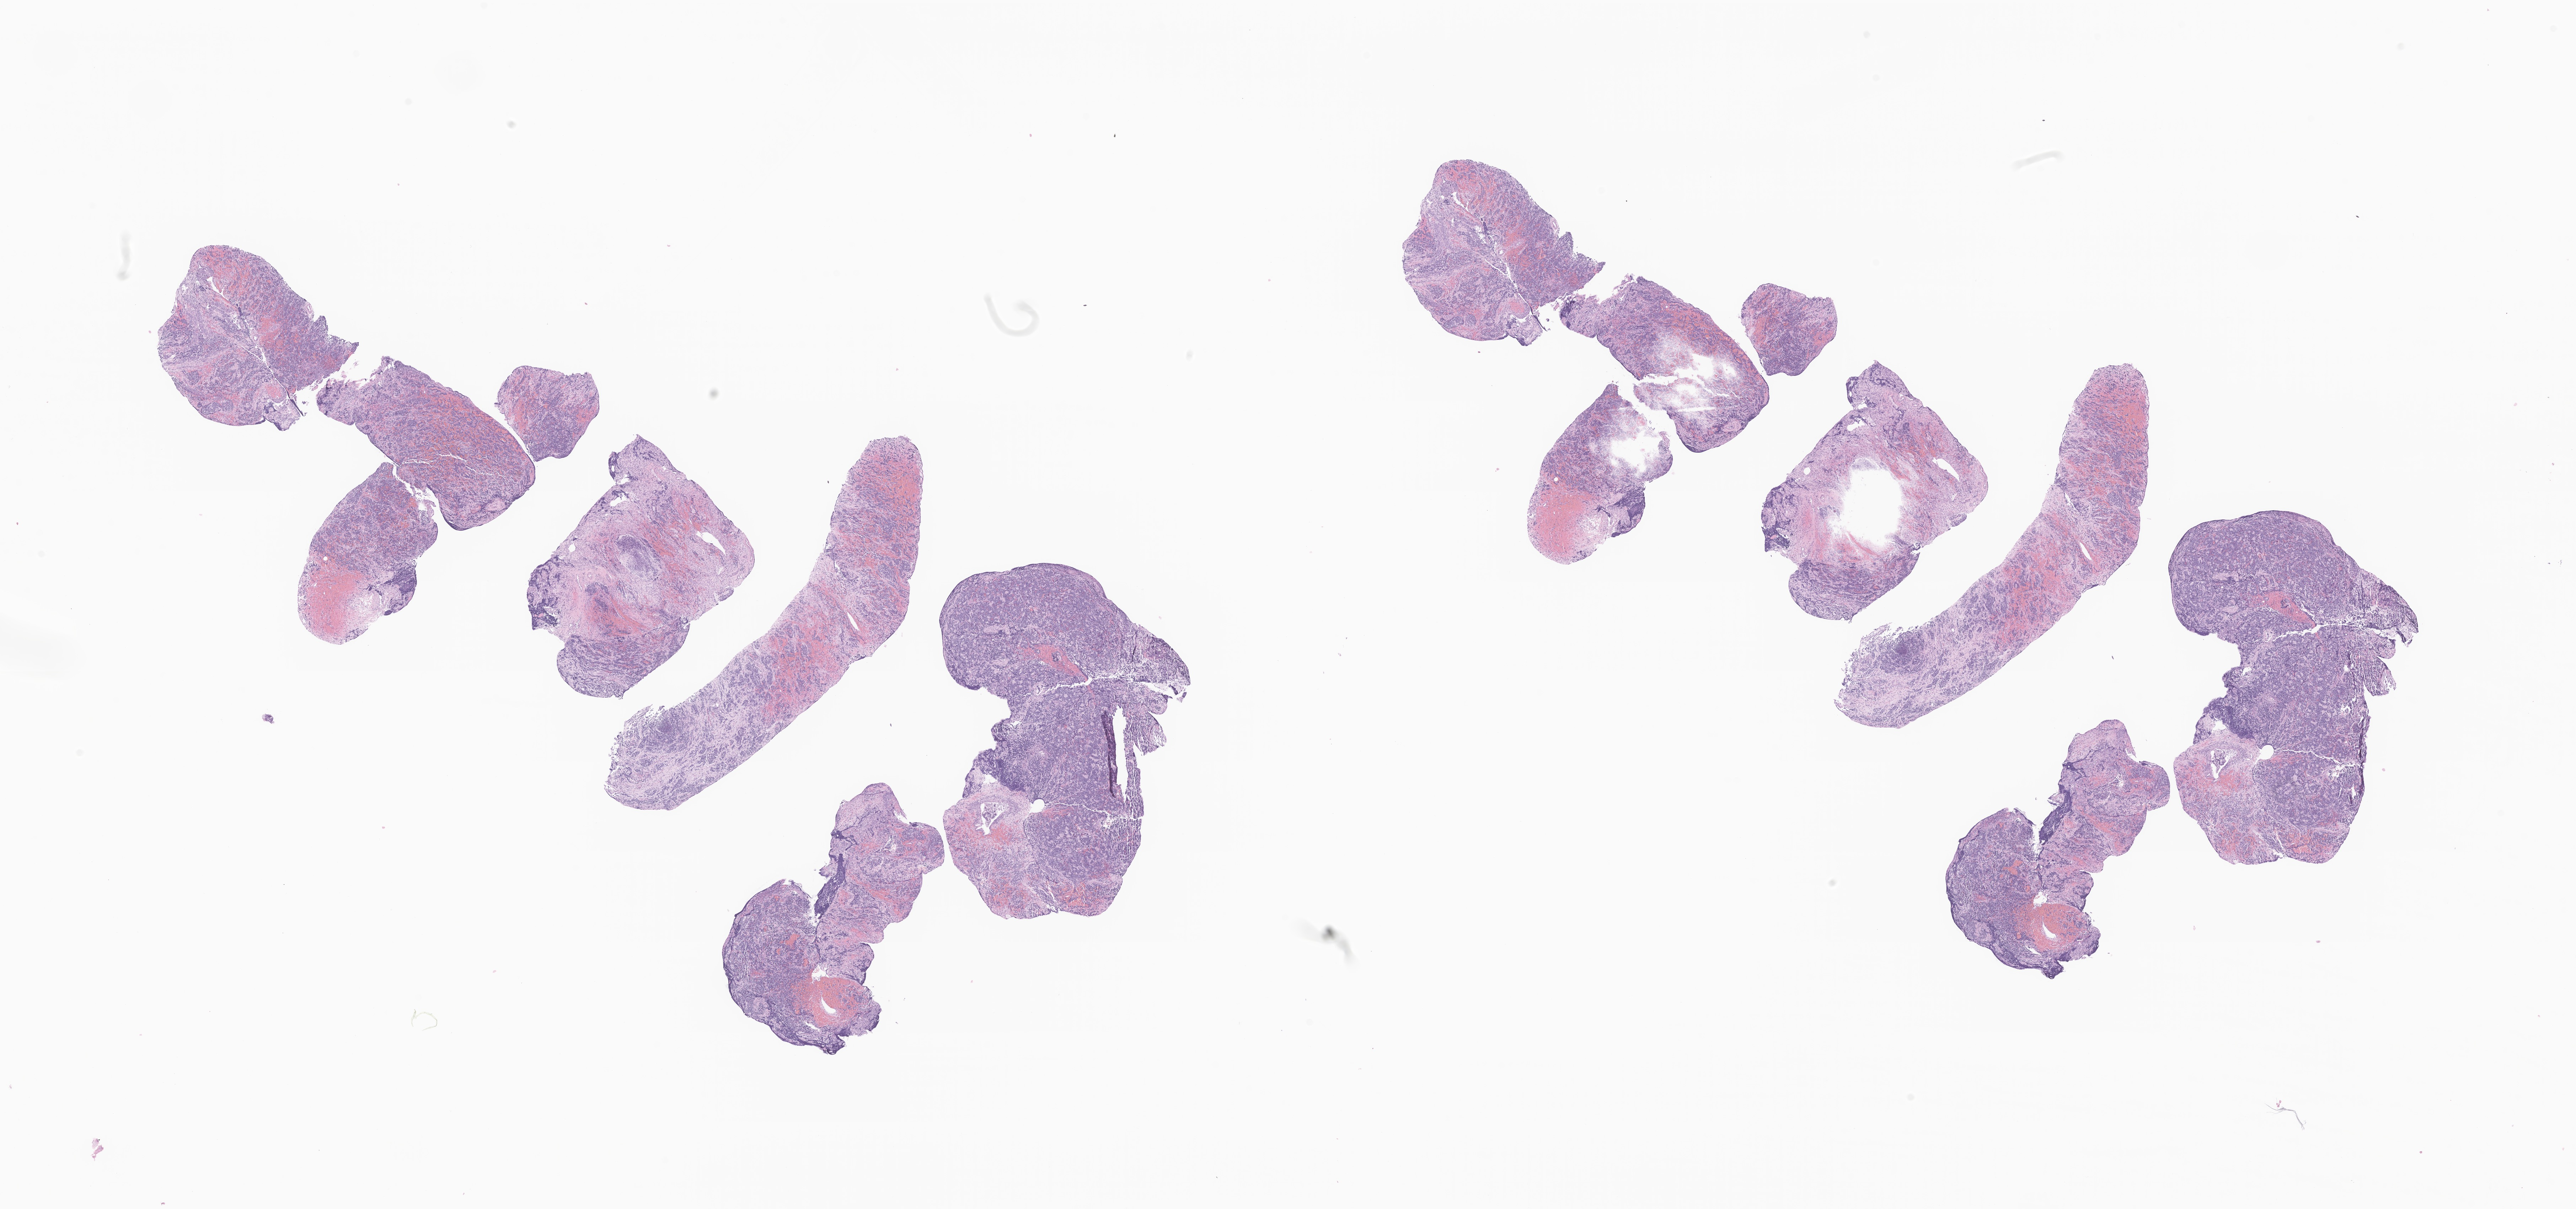
H&E whole-slide image of tumor tissue from the spinal cord — low-resolution overview of the scanned area, about 30.6 x 14.3 mm. Formalin-fixed, paraffin-embedded (FFPE) tissue. Female patient, age 110 days.
Recorded diagnosis: Neuroblastoma, NOS.